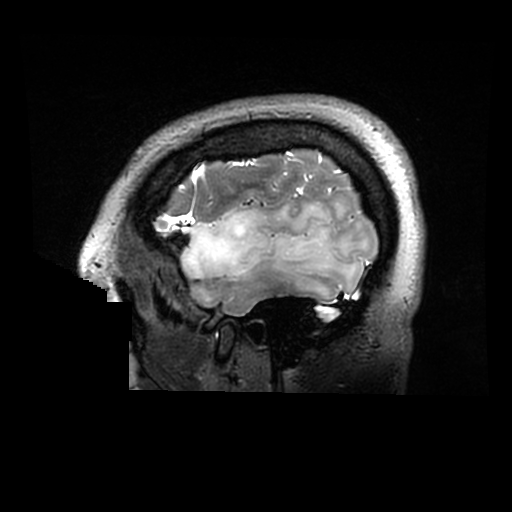
Brain MRI from a brain-tumour surgery series, one sagittal slice; position 243 of 320 along the scan axis; 0.6 mm slice thickness; 512 × 512 image matrix, field of view 240 × 240 mm. From the clinical record (not read from this slice): histopathology: Astrocytoma; WHO grade: 2; IDH mutation: yes.
Annotated regions visible in this slice (expert manual segmentation):
- tumour: bounding box <181,201,360,298> (left, top, right, bottom; pixels)